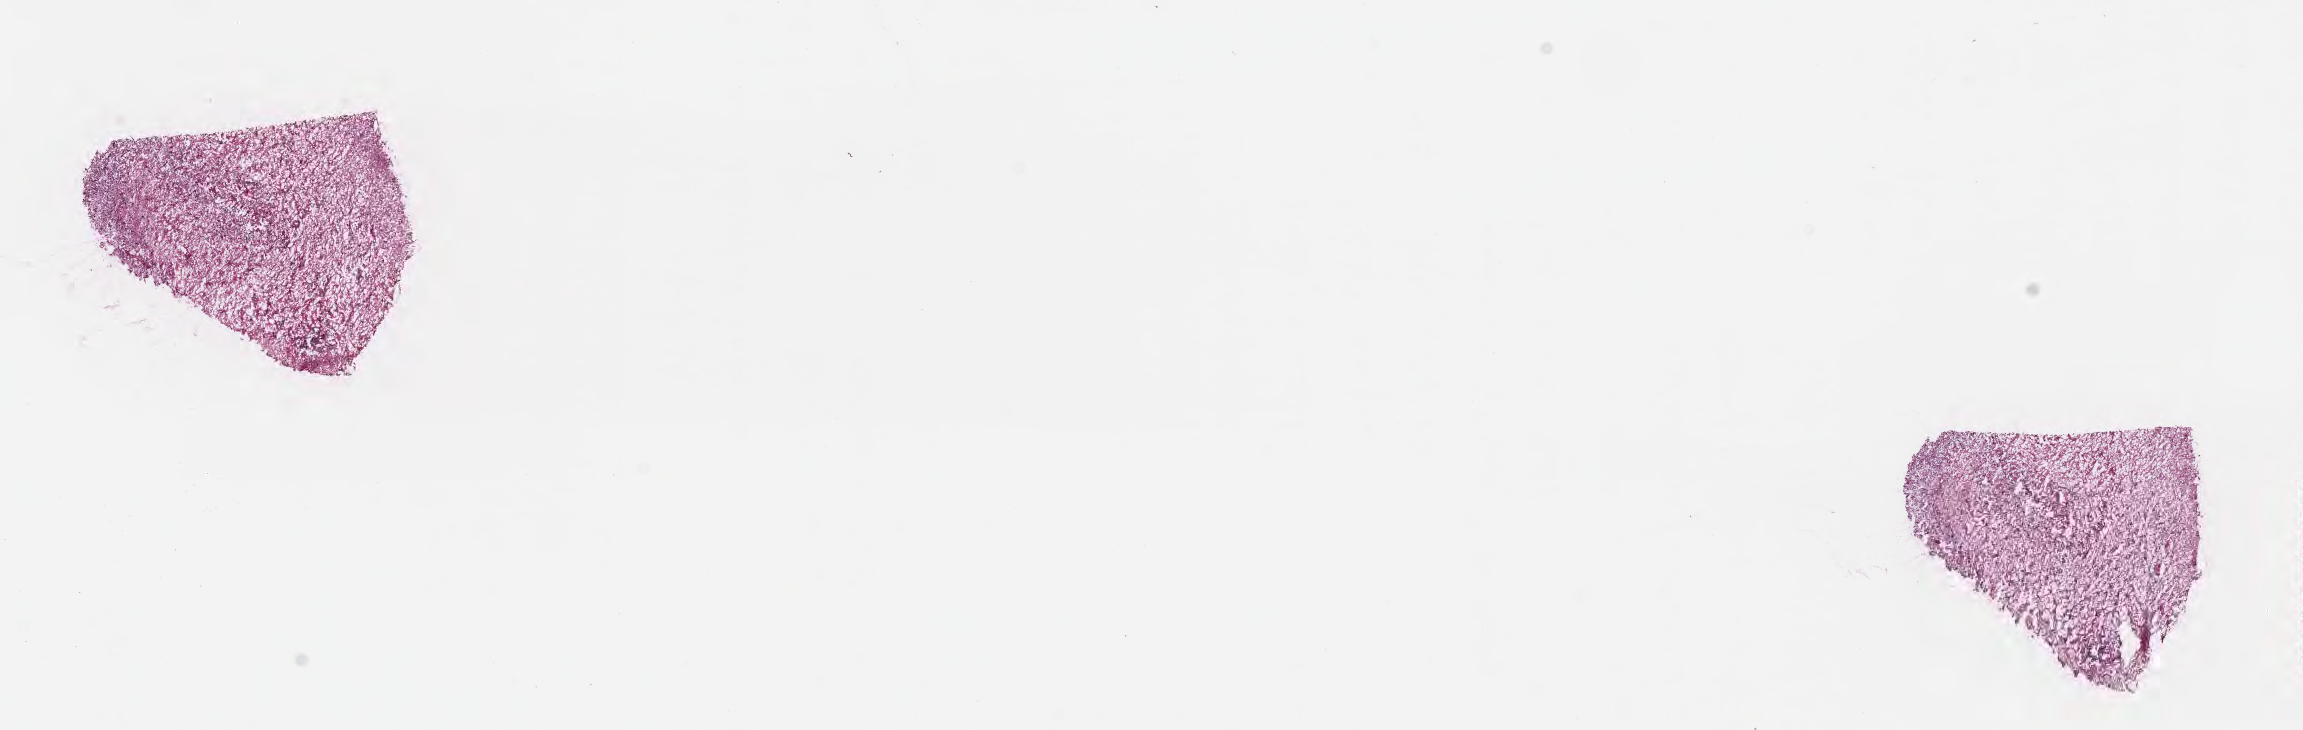
Digitized hematoxylin and eosin (H&E)-stained section, whole scanned area (about 18.6 x 5.9 mm) shown as a low-resolution overview; frozen section (tissue freezing medium); specimen: recurrent tumor; anatomic site: brain. Female patient; age at initial diagnosis 53 years. Composition of this section per pathologist review: tumor cells 47%, tumor nuclei 76%.
Patient diagnosis: Glioblastoma, NOS.